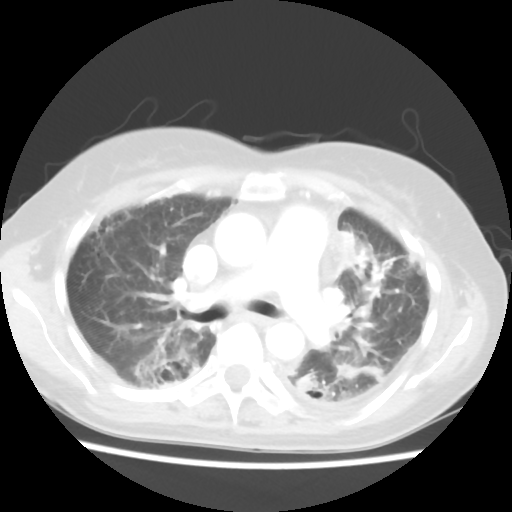
Chest CT, one axial slice; position 37 of 56 along the scan axis; lung window (W 1500 / L -600 HU); 5 mm slice thickness; 512 × 512 image matrix, field of view 309 × 309 mm. Patient: female, 56 years. Case-level facts recorded for this patient, not image findings: clinical TNM (as recorded): T1c N0 M1.
Outlined on this slice (rectangle marked by the reading radiologist):
- lung tumour (recorded histology: adenocarcinoma): bounding box <336,229,368,283> (left, top, right, bottom; pixels)